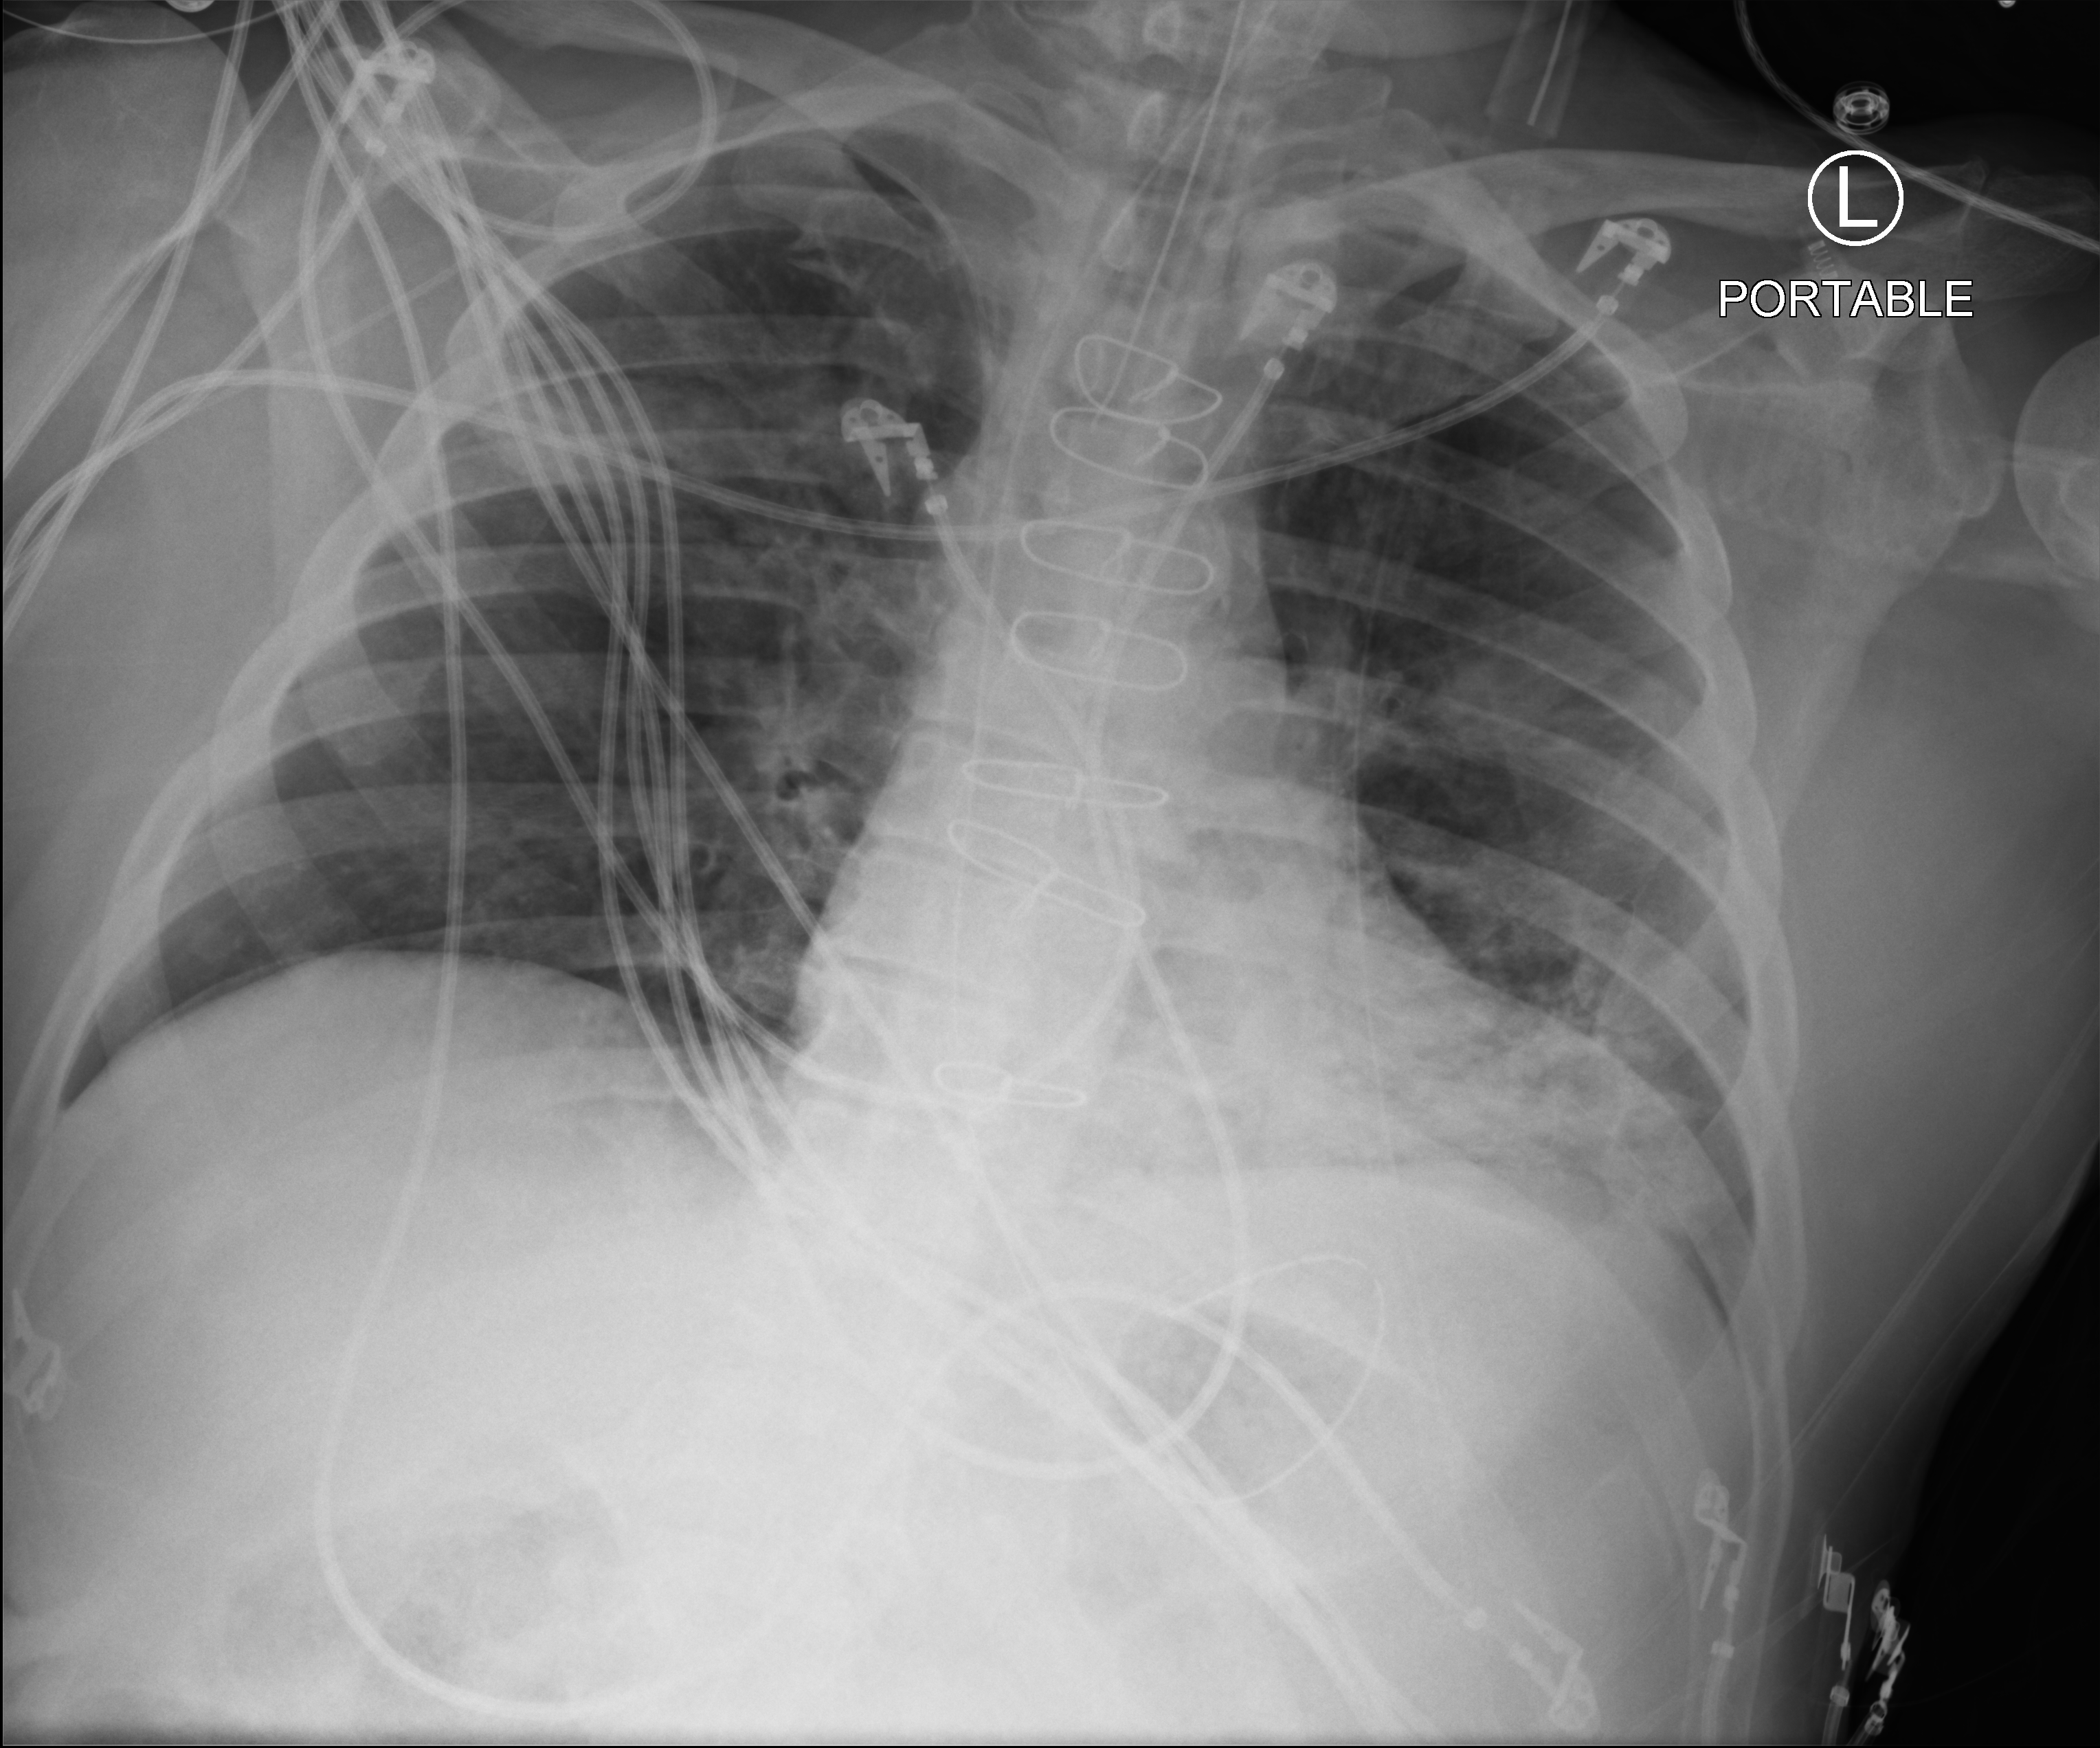
Portable chest radiograph. Male patient hospitalised with COVID-19, age 60–74 years.
Admission-level facts for this patient (not findings on this image; timing relative to this image not recorded): admitted to intensive care during this hospital stay: yes.